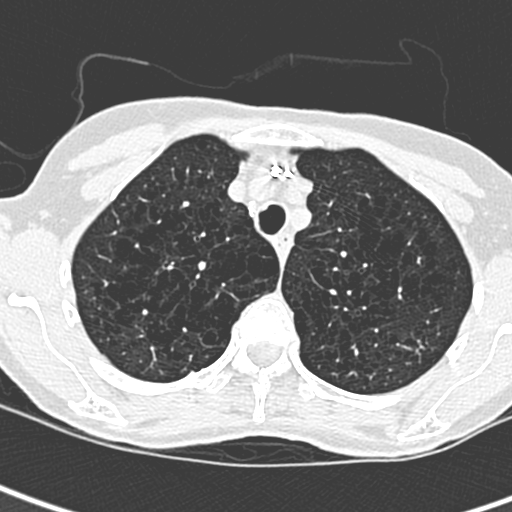
Axial slice from a low-dose chest CT screening exam. Baseline screening round. Lung window (W 1500 / L -600 HU). 1.3 mm slice thickness. Lung (sharp) reconstruction kernel (D). Slice 56 of 259 in the series. 512 × 512 image matrix. Female, age 71 years at enrolment.
• Expert-annotated lung lesion, bounding box <396,330,437,368> (left, top, right, bottom; pixels).
• No non-calcified nodule or mass ≥4 mm was recorded by the screening reader at this exam.
• Official screen result: negative screen, no significant abnormalities.